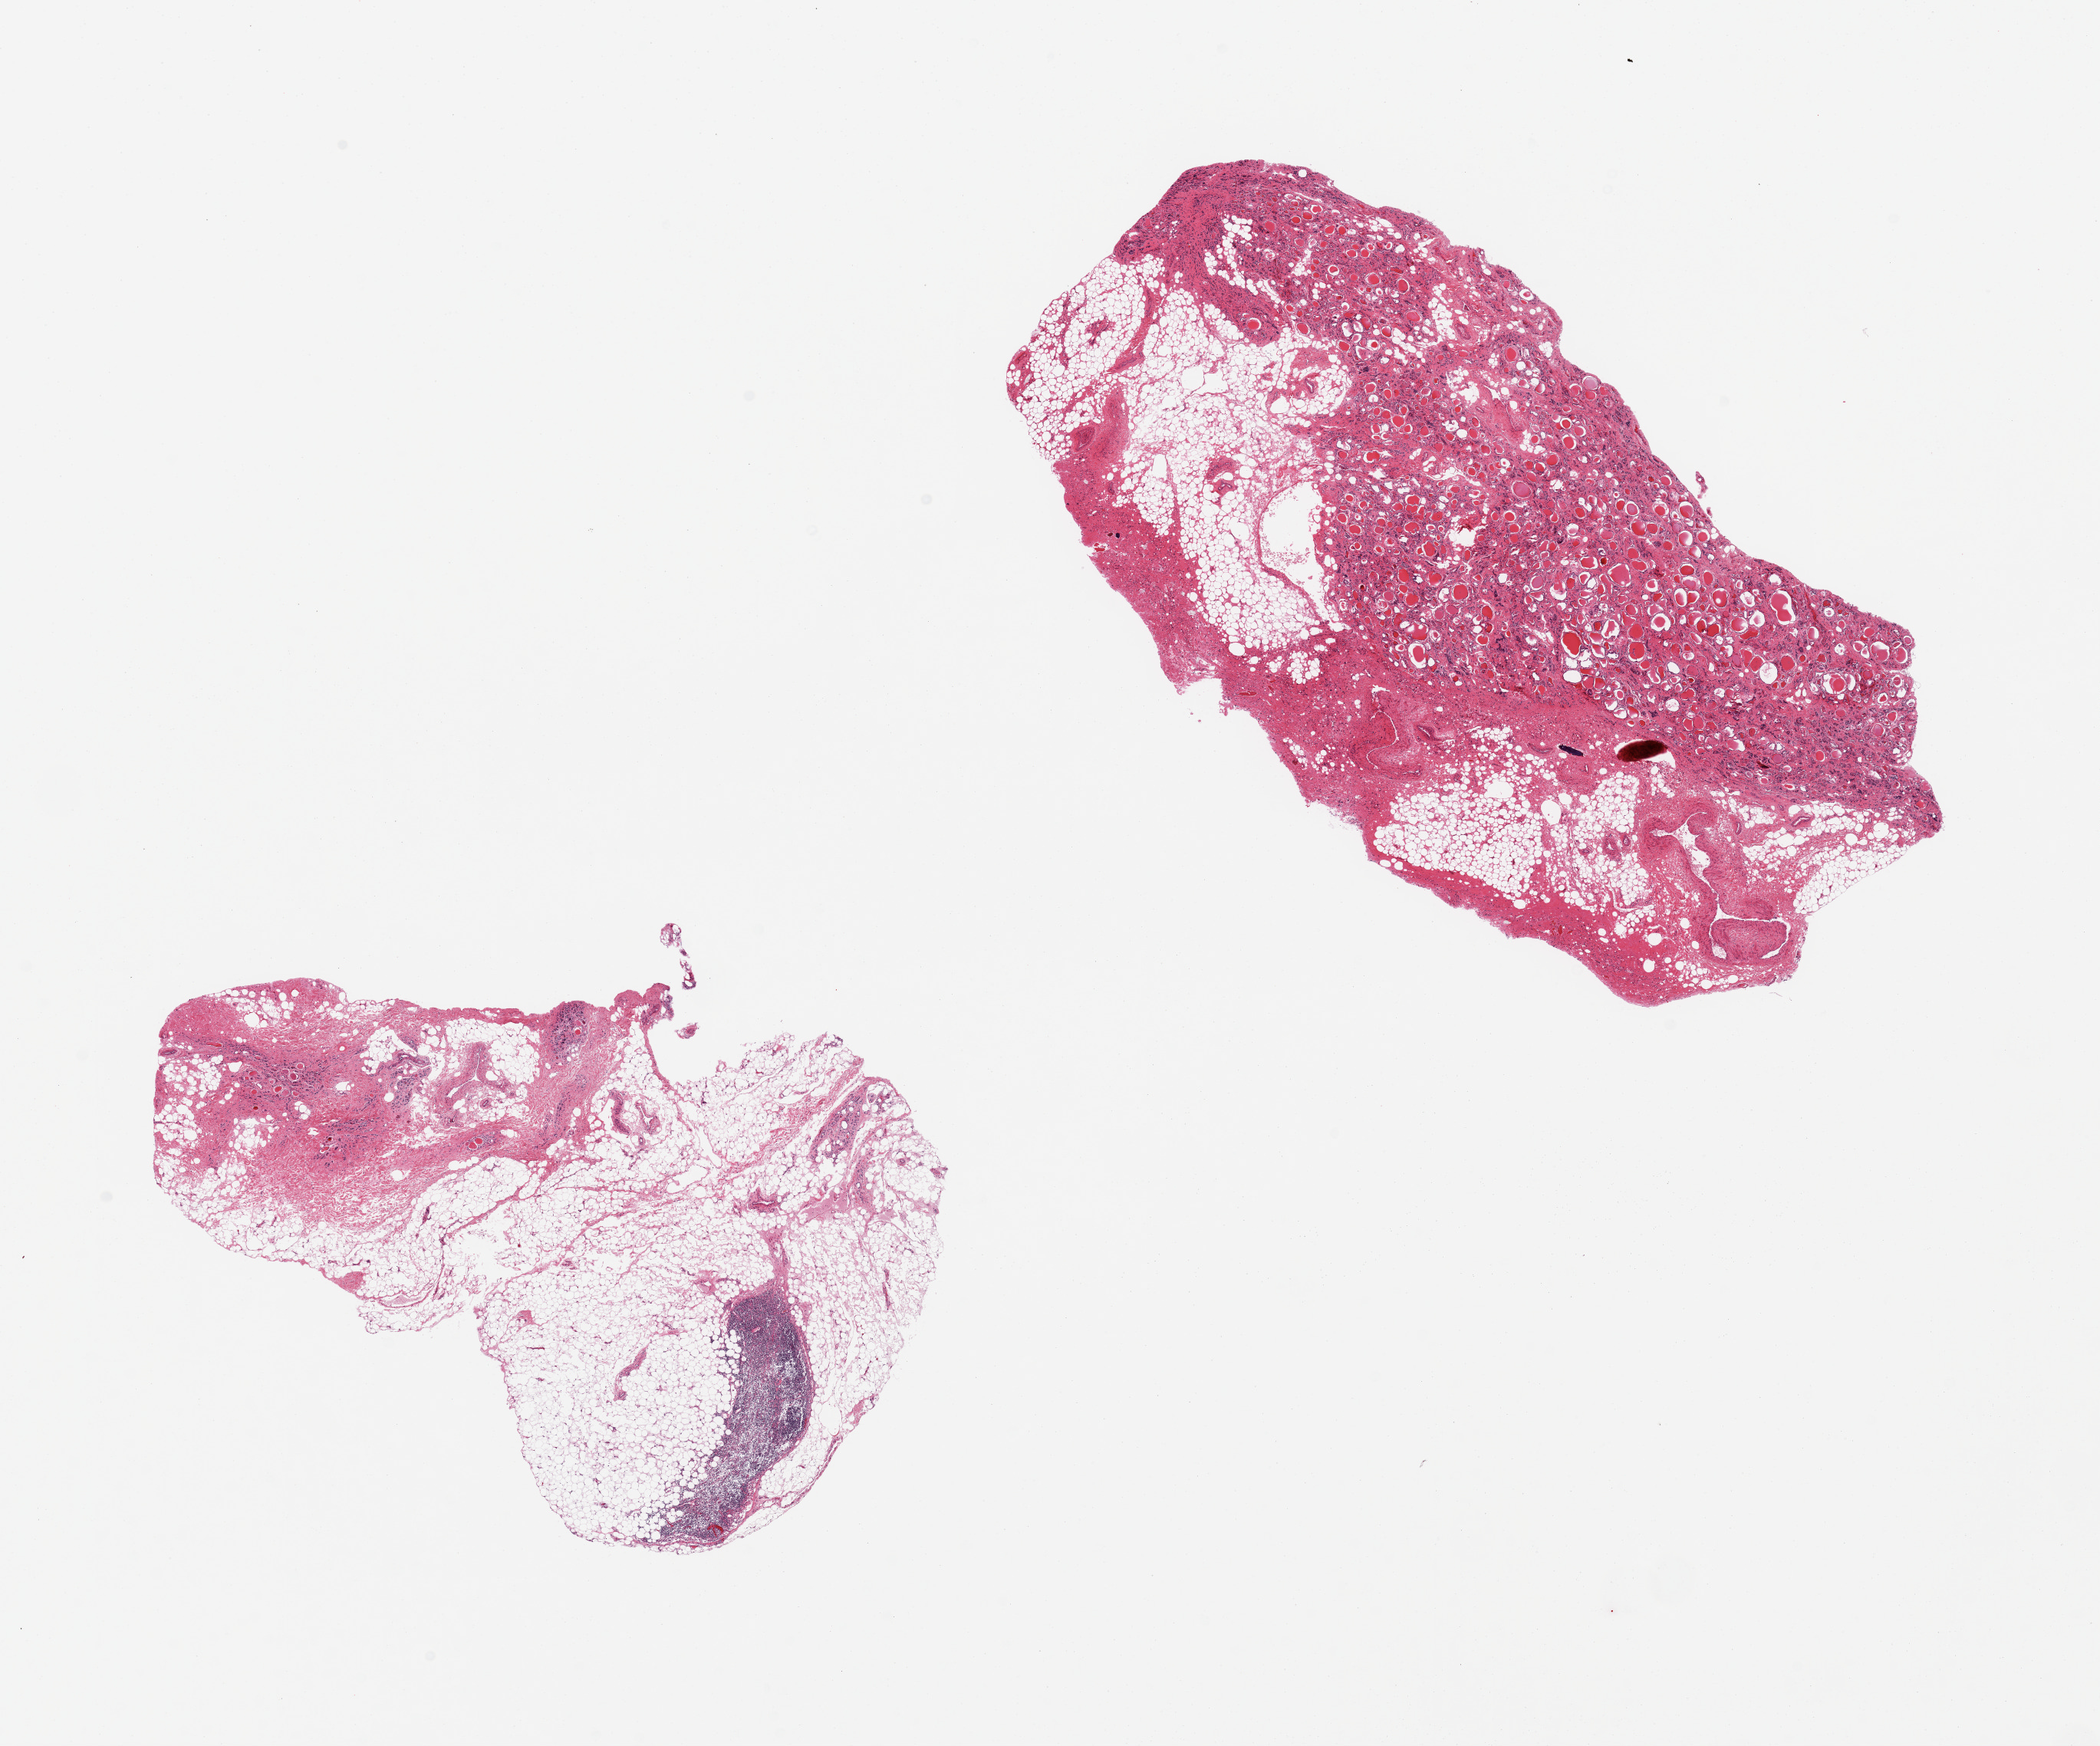
Digitized haematoxylin and eosin-stained section, brightfield — shown as a low-resolution overview of the whole scanned area (about 21.7 x 18.0 mm), PAXgene-fixed, paraffin-embedded tissue, section of thyroid (target tissue), donor tissue sample.
Reviewer comment on this tissue sample: 2 pieces both atrophic with fibrosis, 1 with 50% adjacent fibroadipose tissue; other with 90%adjacent fibroadipose tissue and a lymph node; material of dubious value.